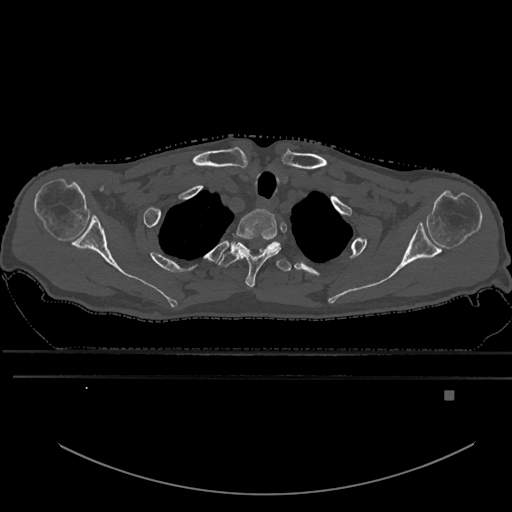
CT including the spine, one axial slice. Position 520 of 969 along the scan axis. Bone window (W 1800 / L 400 HU). 512 × 512 image matrix, field of view 456 × 456 mm. Male patient, age 82 years. Case-level facts recorded for this patient, not image findings: primary cancer: prostate; vertebrae with lytic lesions (as recorded): T11, T9, T8, T2.
Annotated regions visible in this slice (semi-automatically segmented with operator editing):
- T1 vertebra: bounding box (x1, y1, x2, y2) in pixels: (236, 208, 281, 289)
- T2 vertebra: (219, 238, 280, 267)